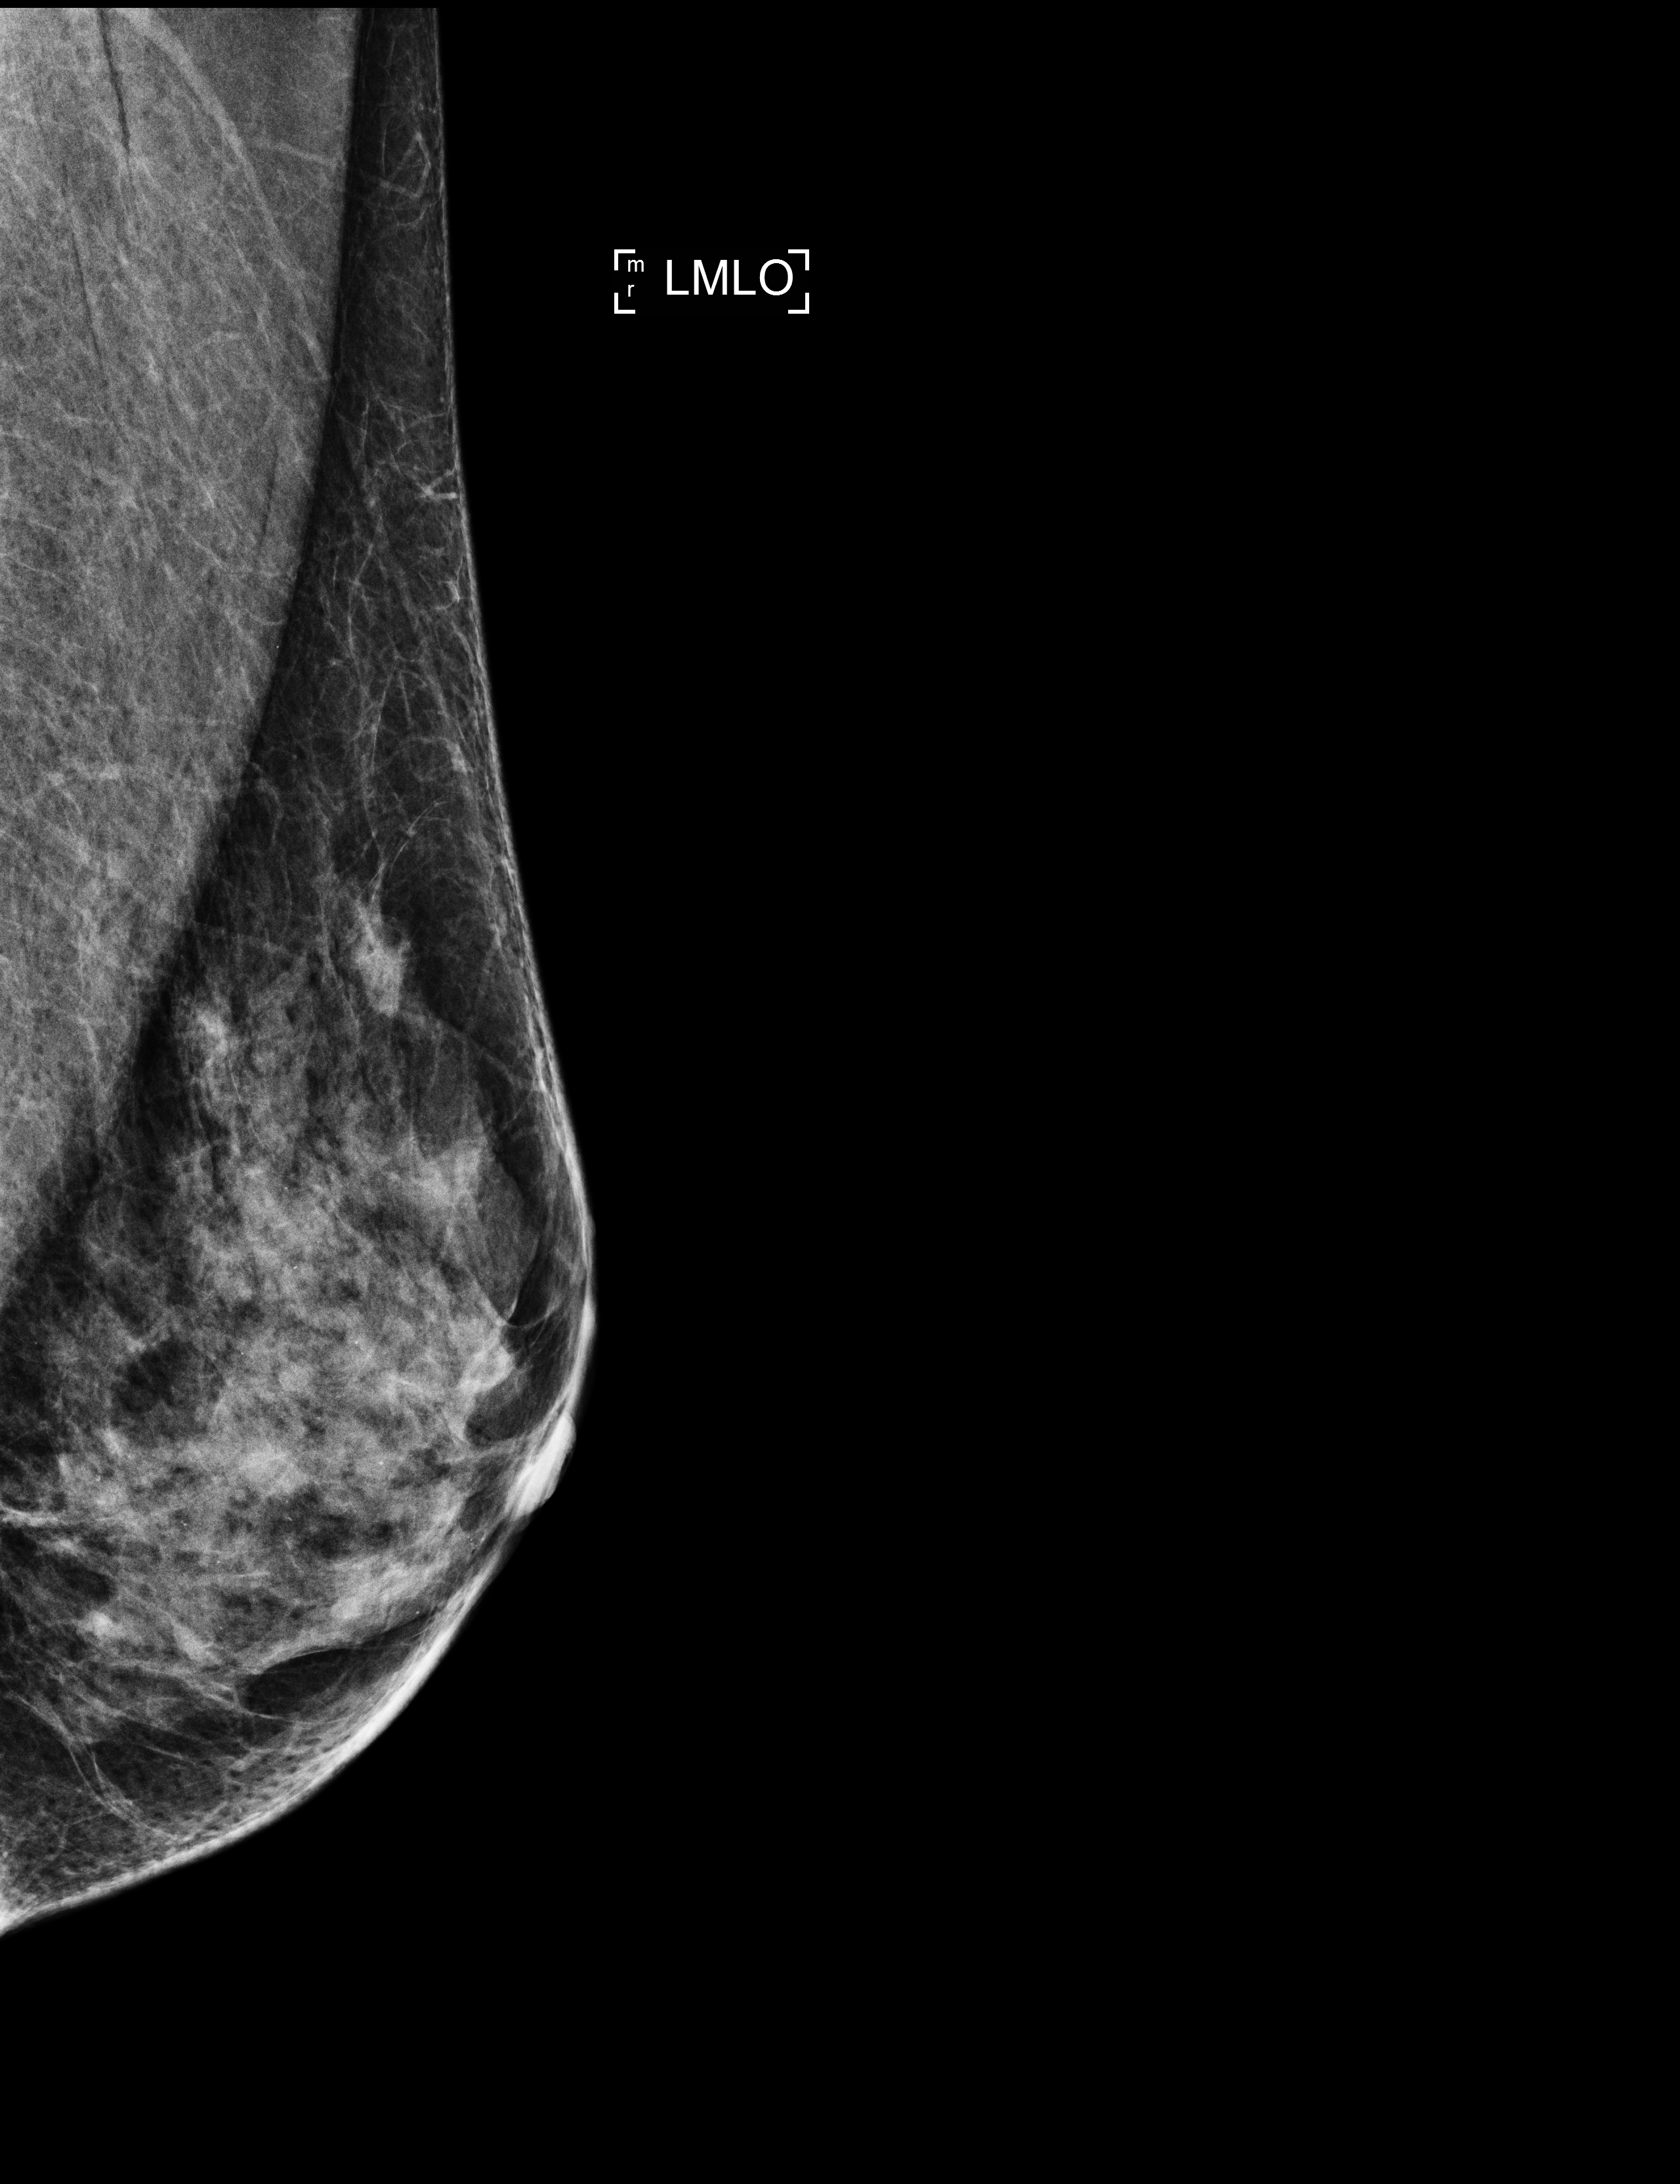
Screening examination, compressed breast thickness 37 mm. Patient: female, 51 years.
Image type: full-field digital mammogram. Breast: left. Projection: mediolateral oblique (MLO) view.